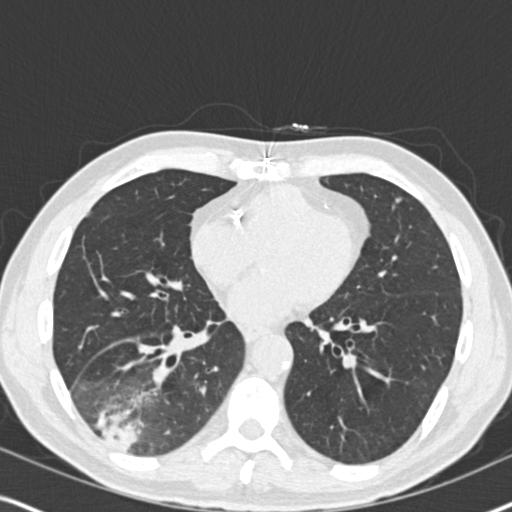
Low-dose screening chest CT, axial slice, second annual screen, lung window (W 1500 / L -600 HU), 2 mm slice thickness. Male, age 61 years at enrolment. Current smoker at enrolment.
Expert reader's lesion annotation, bounding box [x1, y1, x2, y2] px = [61, 342, 193, 467]. Screening reader's record for this exam (one nodule recorded; not confirmed to be the boxed lesion): non-calcified nodule or mass ≥4 mm, right lower lobe, 90 × 80 mm, soft tissue attenuation, pre-existing on the prior screen: yes; interval growth: yes. Later outcome: lung cancer diagnosed 20 days after this screen — bronchiolo-alveolar adenocarcinoma, NOS, right lower lobe, moderately differentiated (G2), stage IIIB (AJCC 6th edition), 90 mm at pathology.